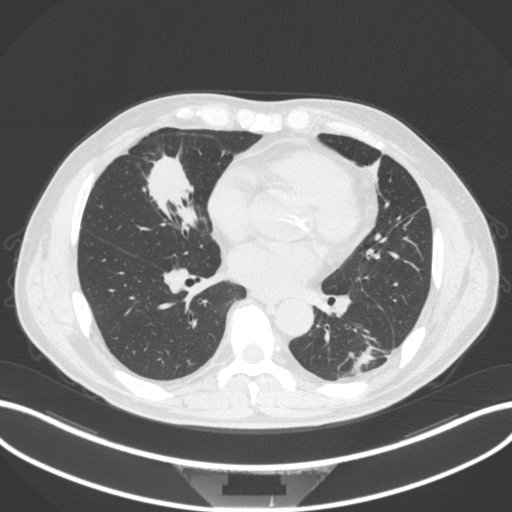
Chest CT, one axial slice. Slice 127 of 399 in the series (ordered by position). Reconstruction kernel B31f. 120 kVp. Lung window (W 1500 / L -600 HU). 1 mm slice thickness. 512 × 512 image matrix. Patient: male, 59 years. From the clinical record (not read from this slice): clinical TNM (as recorded): T2a N1 M0.
Structures marked on this image (bounding box drawn by a radiologist):
- lung tumour (recorded histology: adenocarcinoma): bounding box <140,145,201,221> (left, top, right, bottom; pixels)